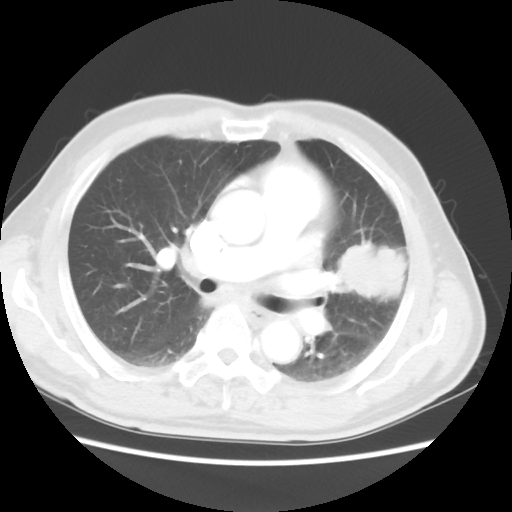
Chest CT, one axial slice; slice 29 of 50 in the series (ordered by position); 120 kVp; lung window (W 1500 / L -600 HU); 5 mm slice thickness; 512 × 512 image matrix, field of view 360 × 360 mm. Patient: male, 69 years. From the clinical record (not read from this slice): clinical TNM (as recorded): T3 N1 M1a.
Outlined on this slice (bounding box drawn by a radiologist):
- lung tumour (recorded histology: squamous cell carcinoma): bounding box <330,226,422,326> (left, top, right, bottom; pixels)